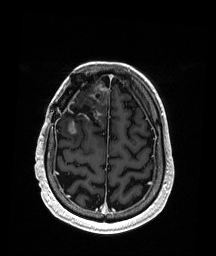
Brain MRI from a brain-tumour surgery series, one axial slice; slice 48 of 192 in the series (ordered by position); T1-weighted post-contrast; 1 mm slice thickness; 216 × 256 image matrix. Case-level facts recorded for this patient, not image findings: histopathology: Astrocytoma; WHO grade: 3; IDH mutation: yes; tumour location: Right Frontal.
Annotated regions visible in this slice (expert manual segmentation):
- previous resection cavity: bounding box <65,93,101,126> (left, top, right, bottom; pixels)
- tumour: <69,85,109,134>